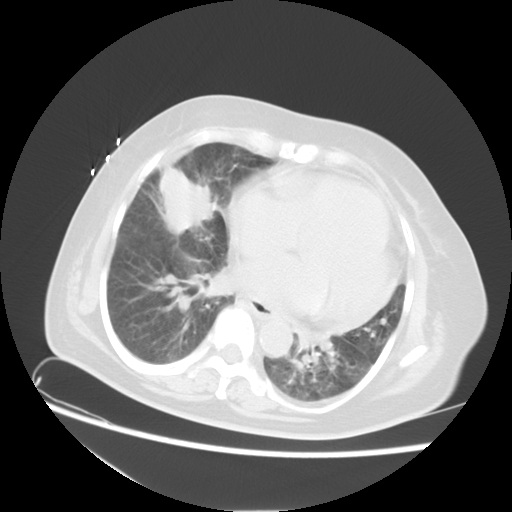
Chest CT, one axial slice; reconstruction kernel STANDARD; lung window (W 1500 / L -600 HU); 512 × 512 image matrix, field of view 350 × 350 mm. Female patient, age 67 years. From the clinical record (not read from this slice): clinical TNM (as recorded): T2a N3 M1a.
Structures marked on this image (rectangle marked by the reading radiologist):
- lung tumour (recorded histology: adenocarcinoma): bounding box <155,160,222,238> (left, top, right, bottom; pixels)